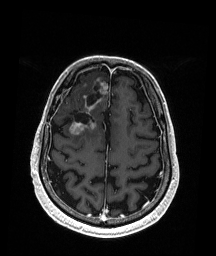
Brain MRI from a brain-tumour surgery series, one axial slice. Position 56 of 192 along the scan axis. T1-weighted post-contrast. 1 mm slice thickness. 216 × 256 image matrix. Case-level facts recorded for this patient, not image findings: histopathology: Astrocytoma; WHO grade: 3; IDH mutation: yes; tumour location: Right Frontal.
Outlined on this slice (expert manual segmentation):
- previous resection cavity: bounding box <69,87,100,124> (left, top, right, bottom; pixels)
- tumour: <69,83,108,136>